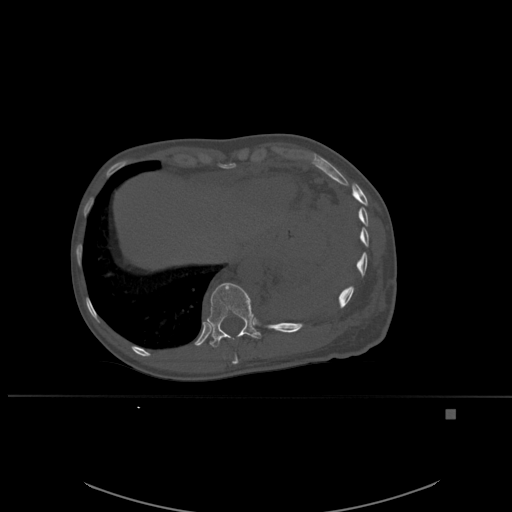
CT including the spine, one axial slice; bone window (W 1800 / L 400 HU); 1.5 mm slice thickness; 512 × 512 image matrix, field of view 440 × 440 mm. Patient: female, 45 years. From the clinical record (not read from this slice): primary cancer: lung.
Outlined on this slice (semi-automatically segmented with operator editing):
- T10 vertebra: bounding box [x1, y1, x2, y2] px = [232, 354, 238, 365]
- T11 vertebra: [207, 282, 261, 348]